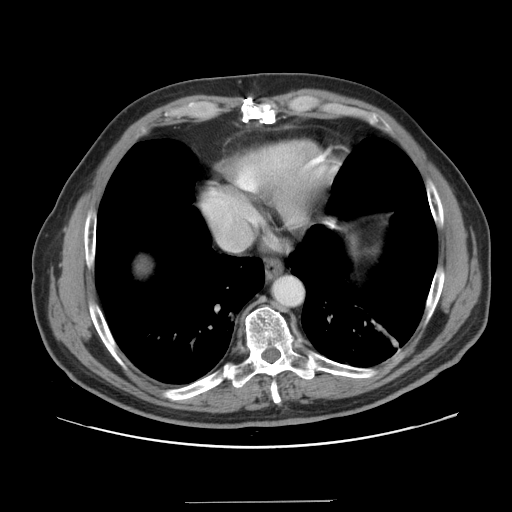
Contrast-enhanced abdominal CT, one axial slice. Slice 147 of 151 in the series (ordered by position). 120 kVp. Intravenous contrast given. Soft-tissue window (W 400 / L 40 HU). 2.5 mm slice thickness. 512 × 512 image matrix. Male patient, age 63 years. From the clinical record (not read from this slice): diagnosis: colorectal cancer liver metastases, imaged before liver resection; multiple liver metastases: no; largest metastasis: 2.1 cm.
Structures marked on this image (outlined manually by an expert reader):
- liver: bounding box [x1, y1, x2, y2] px = [134, 255, 151, 273]
- planned liver remnant (the part of the liver to remain after resection): [134, 253, 151, 273]